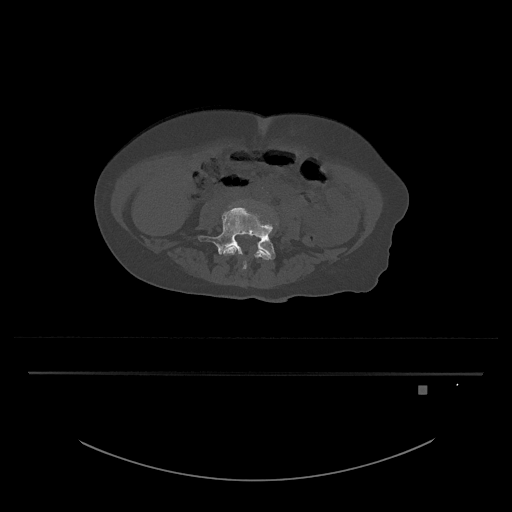
CT including the spine, one axial slice; position 326 of 797 along the scan axis; reconstruction kernel Br40s/3; bone window (W 1800 / L 400 HU); 0.5 mm slice thickness; 512 × 512 image matrix. Patient: female, 57 years. Case-level facts recorded for this patient, not image findings: primary cancer: cervical.
Annotated regions visible in this slice (semi-automatic segmentation, software-assisted and operator-edited):
- L4 vertebra: box from (x=223, y=246) to (x=271, y=272) px